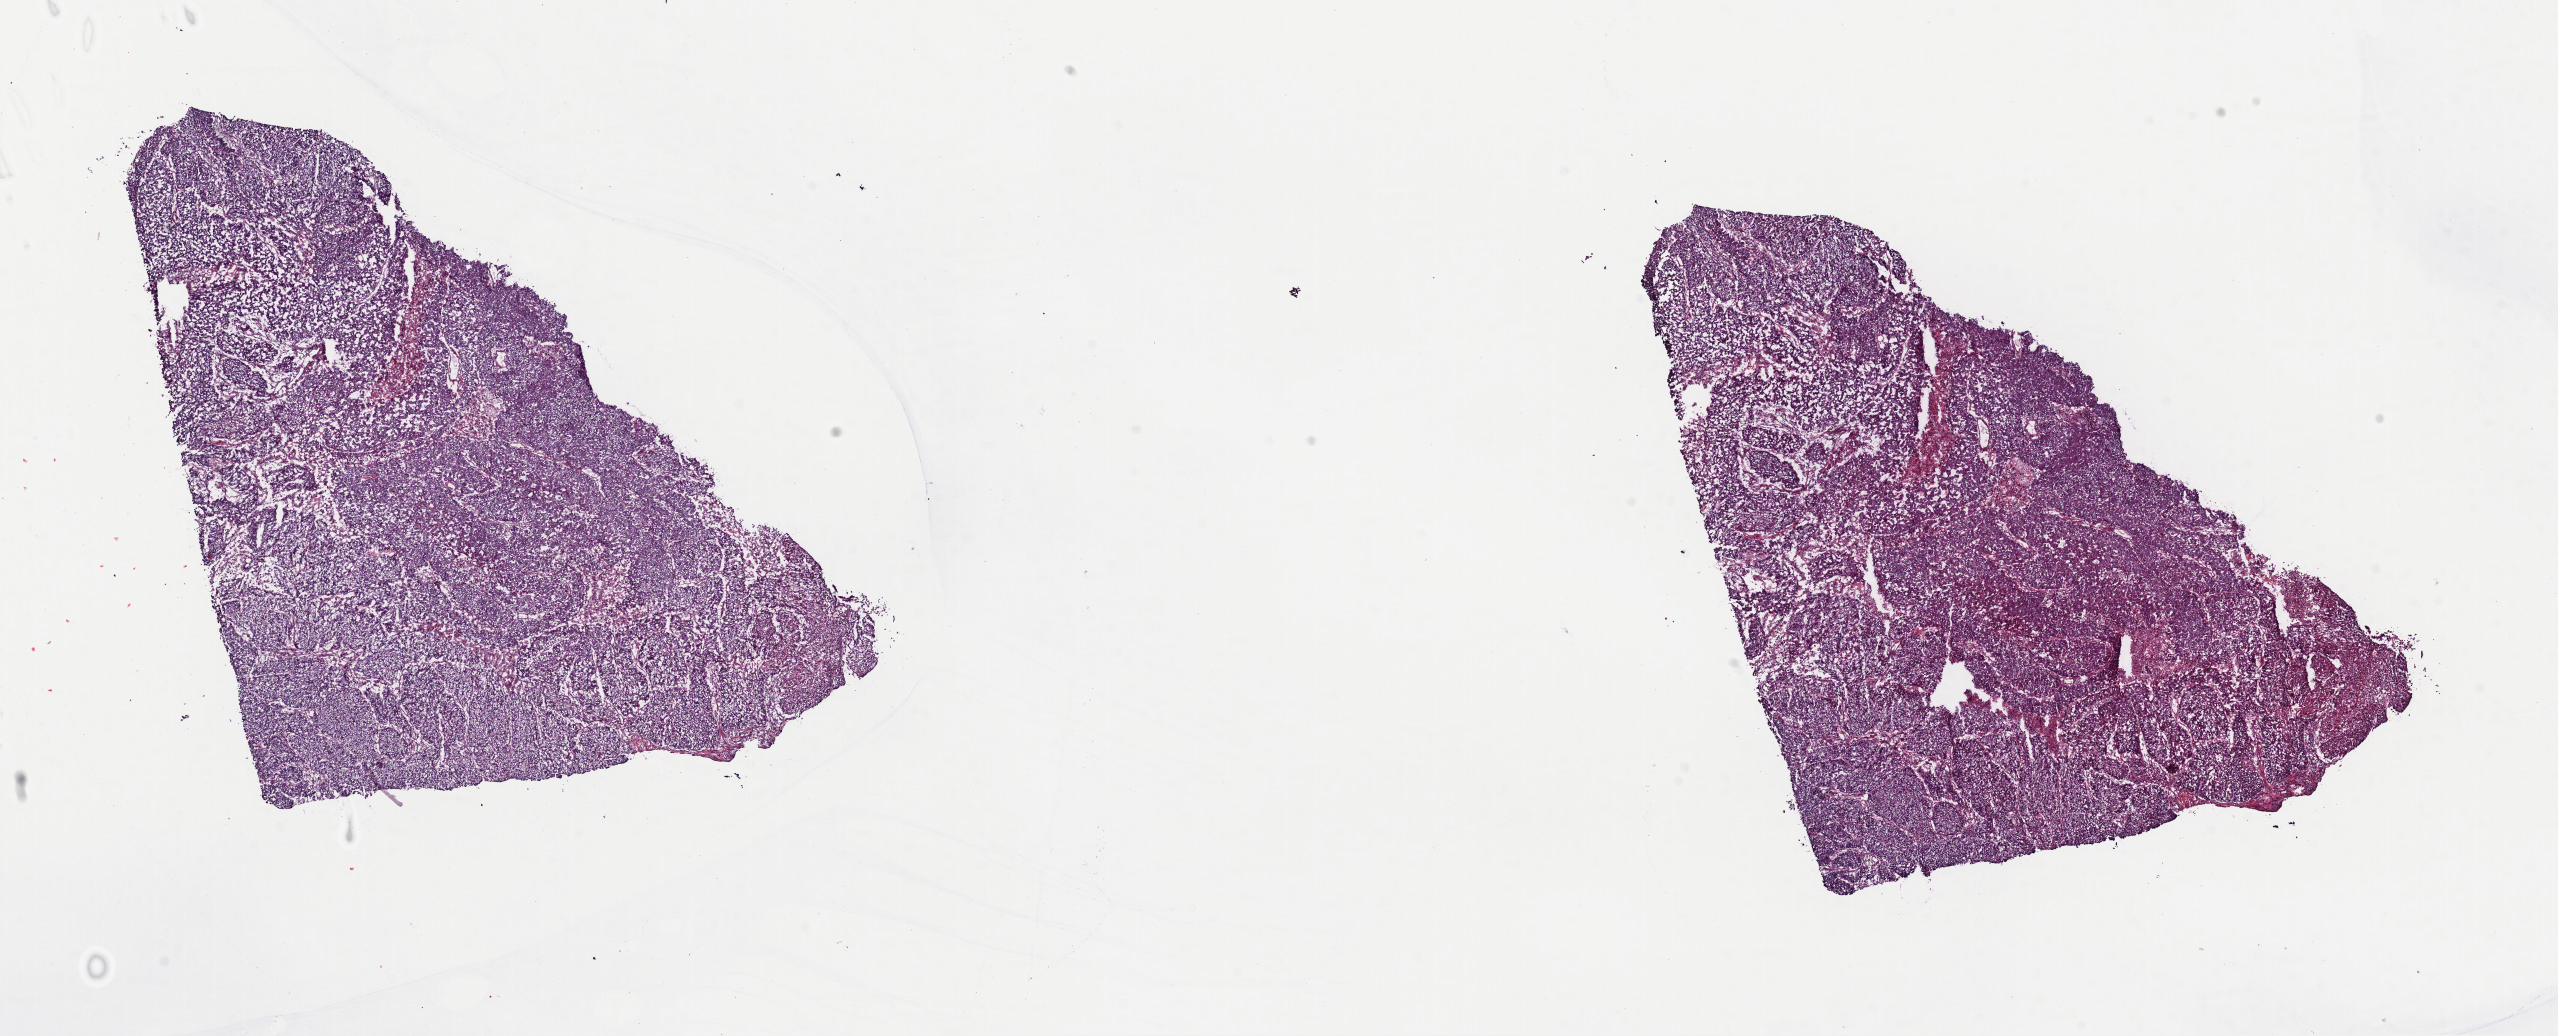
Whole-slide histology image, Hematoxylin and eosin (H&E) stained — a low-resolution overview of the entire scanned area, about 20.2 x 8.2 mm (acquisition: 40x scan), frozen section from the top of the tissue portion, sample: primary tumour, lung. Male patient; age at initial diagnosis 53 years. Pathologist review of this section (percent, as recorded): tumour cells 95%, tumour nuclei 95%, normal cells 0%, stromal cells 0%, necrosis 5%. Inflammatory infiltration, as recorded: lymphocyte infiltration 0%, monocyte infiltration 0%, neutrophil infiltration 0%.
* AJCC pathologic stage: IIB (7th edition)
* diagnosis: Squamous cell carcinoma, NOS (upper lobe, lung)
* TNM: T3 N0 M0